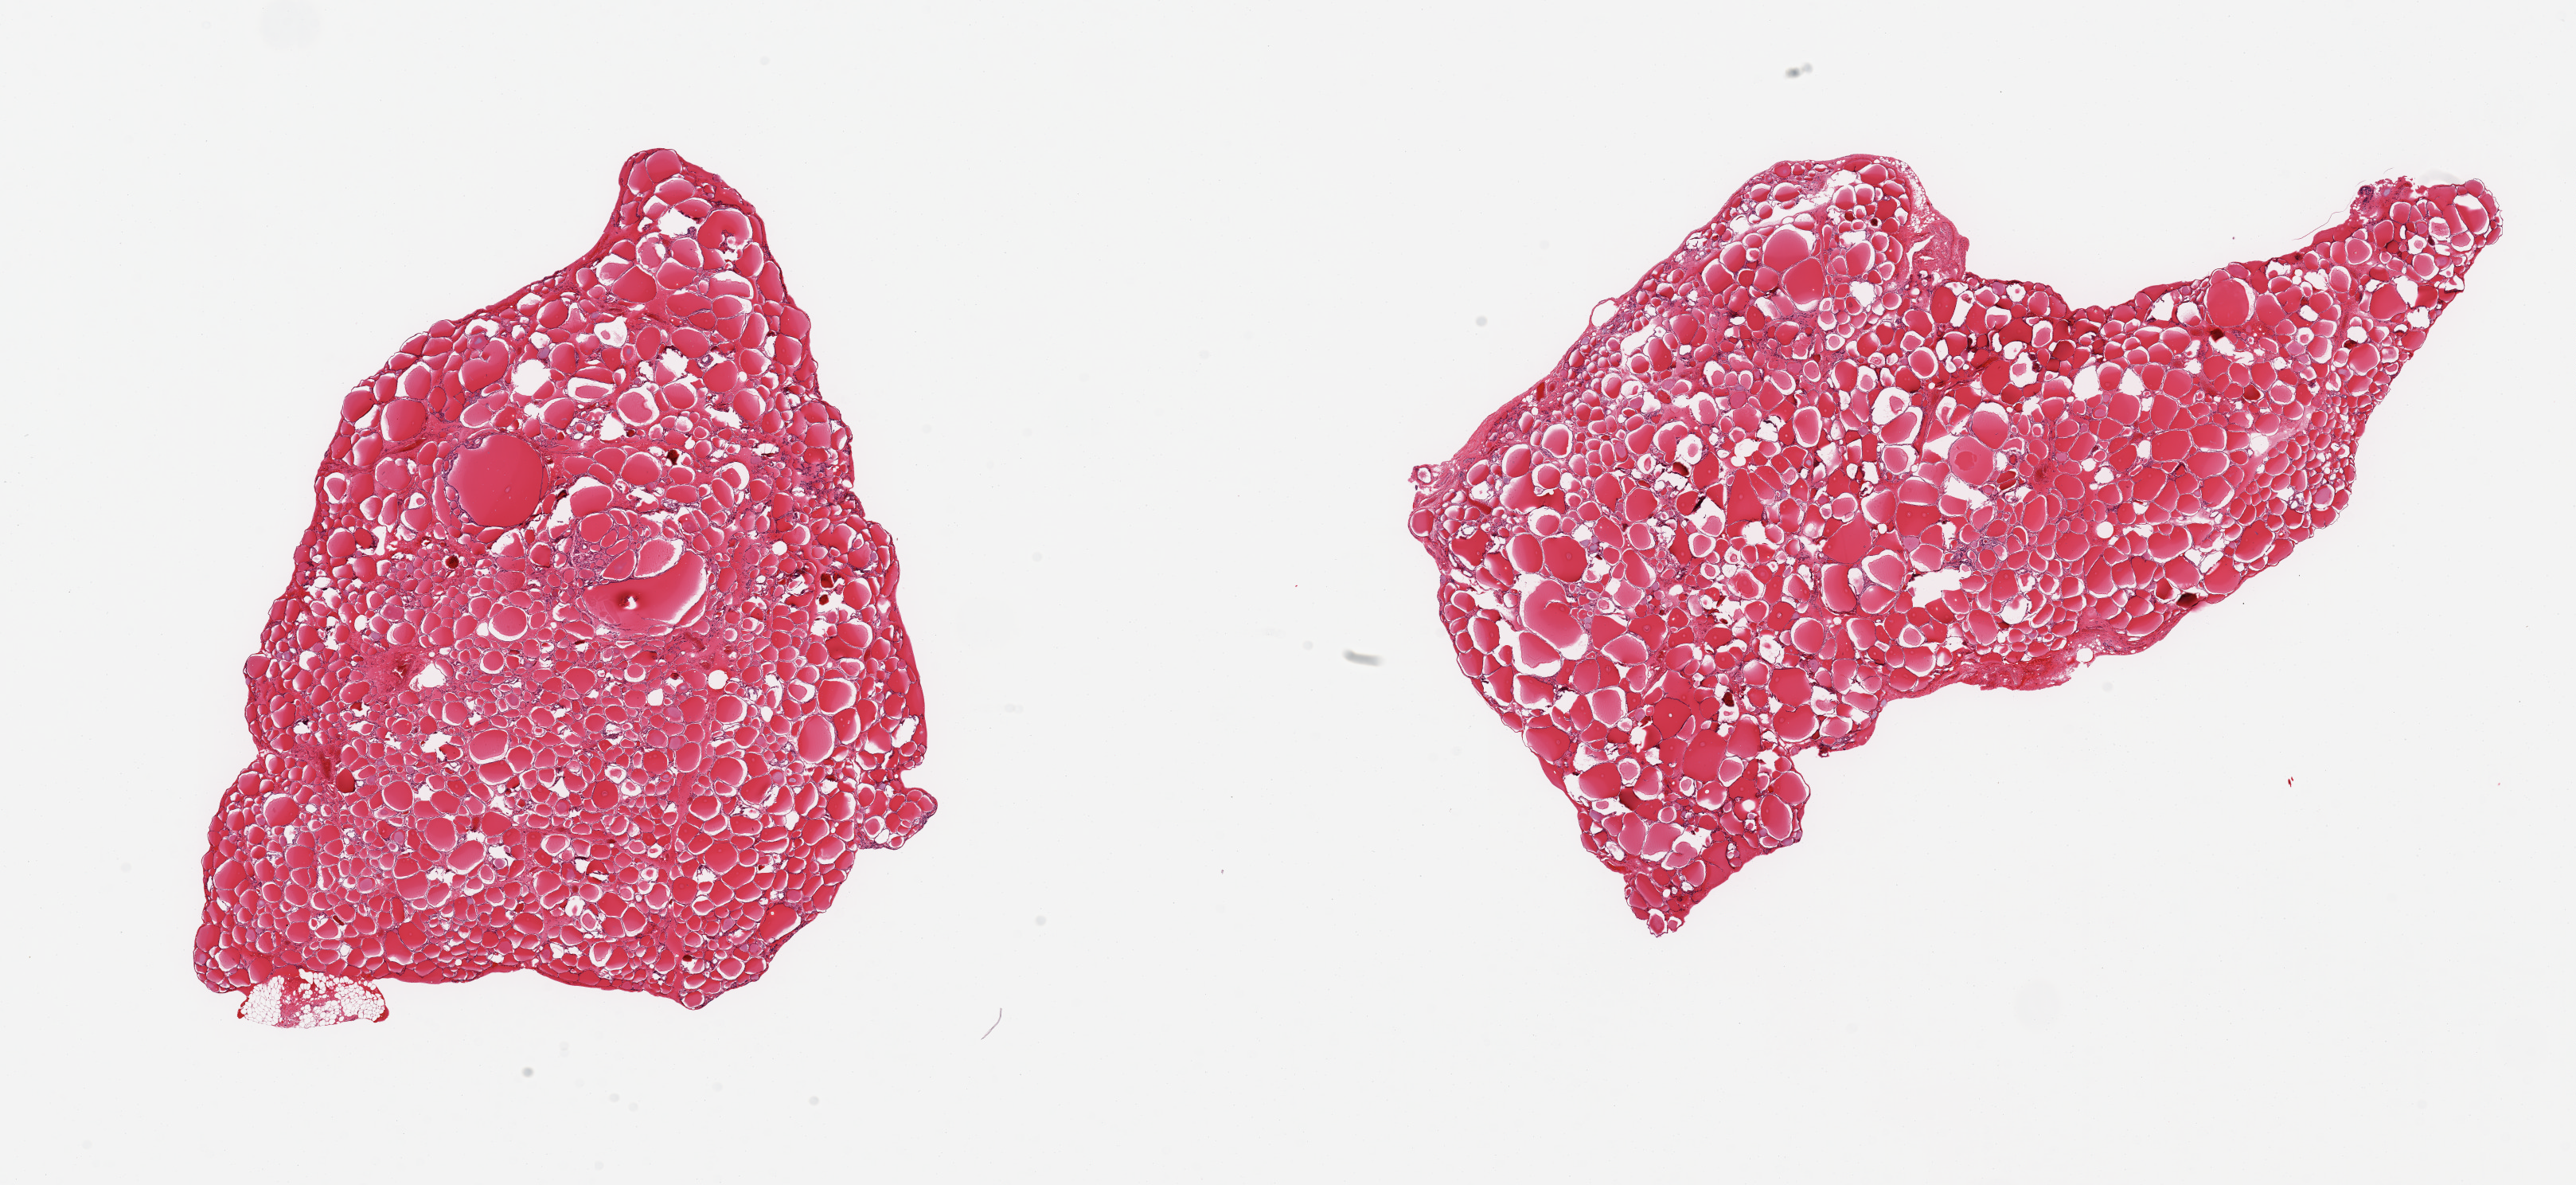
Digitized hematoxylin and eosin (H&E)-stained section, low-resolution overview of the scanned area, about 25.6 x 11.8 mm; PAXgene-fixed, paraffin-embedded tissue; sampled site (target tissue): thyroid; donor tissue sample.
Review note (as recorded): 2 pieces; minmal extraneous tissue.